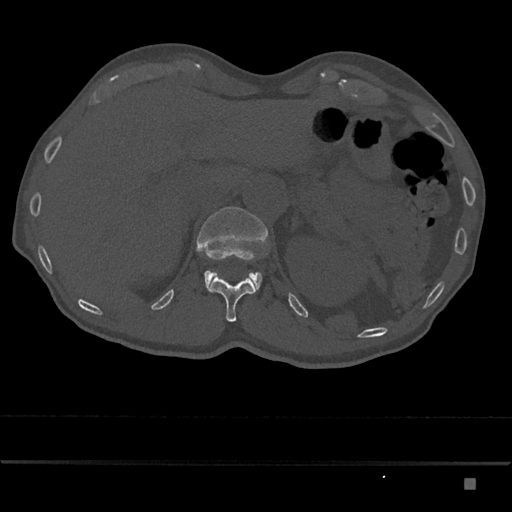
CT including the spine, one axial slice. Slice 586 of 797 in the series (ordered by position). Bone window (W 1800 / L 400 HU). 512 × 512 image matrix, field of view 390 × 390 mm. Patient: male, 72 years. From the clinical record (not read from this slice): primary cancer: prostate.
Structures marked on this image (semi-automatically segmented with operator editing):
- L1 vertebra: bounding box [x1, y1, x2, y2] px = [196, 207, 268, 291]
- T12 vertebra: [207, 276, 256, 322]